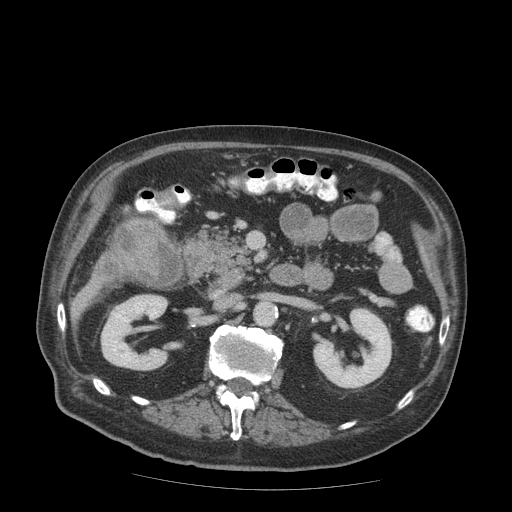
Contrast-enhanced abdominal CT (liver protocol), one axial slice; position 24 of 99 along the scan axis; soft-tissue window (W 400 / L 40 HU); 2.5 mm slice thickness; 512 × 512 image matrix, field of view 420 × 420 mm. From the clinical record (not read from this slice): diagnosis: hepatocellular carcinoma (patient treated with transarterial chemoembolisation; whether this scan precedes or follows treatment is not stated here); TNM stage (as recorded): Stage-IIIB; Child-Pugh class: A; tumour differentiation: well differentiated; tumour nodularity: multinodular.
Outlined on this slice (semi-automatic segmentation, software-assisted and operator-edited):
- liver parenchyma outside the tumour (the mass and vessels are separate outlines, so this box may not span the whole liver): bounding box [x1, y1, x2, y2] px = [124, 218, 136, 228]
- mass: [91, 220, 167, 288]